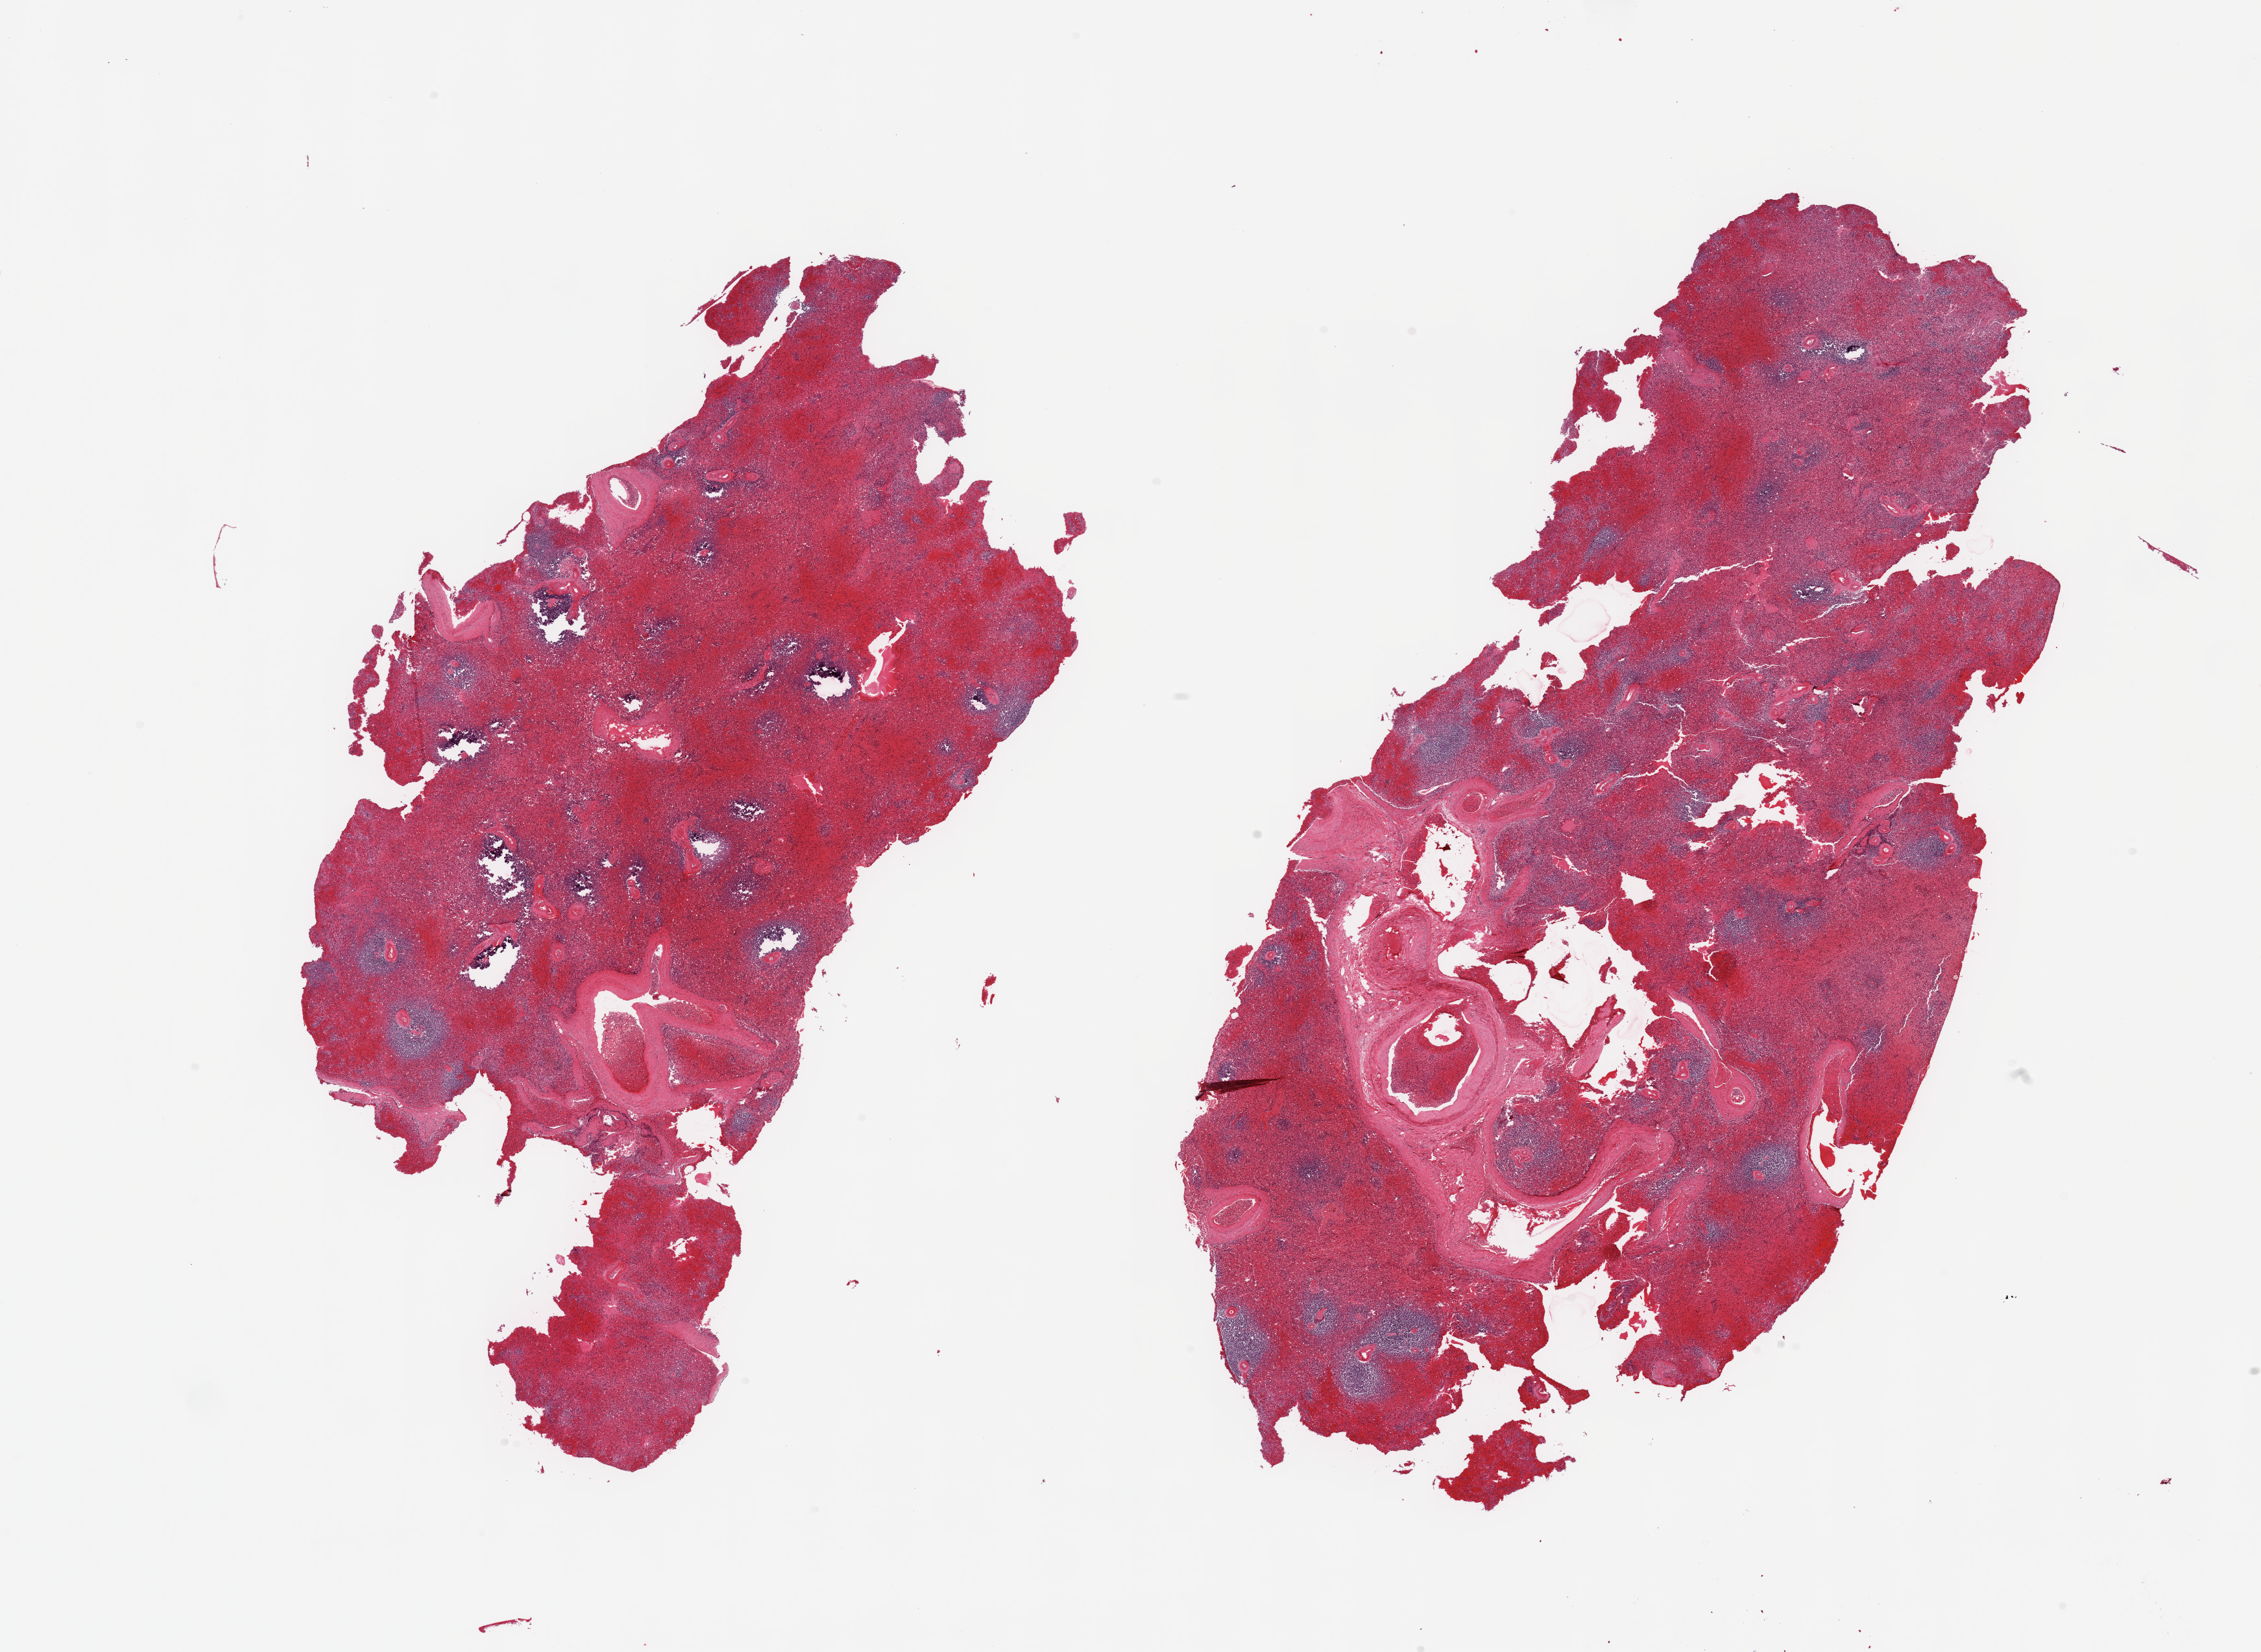
Whole-slide image, haematoxylin and eosin stain, brightfield, shown as a low-resolution overview of the whole scanned area (about 27.6 x 20.1 mm); PAXgene-fixed, paraffin-embedded tissue; section of spleen (target tissue); tissue donor sample. Donor sex: male.
Pathologist's review note for this sample: 2 pieces, moderate - marked congestion.